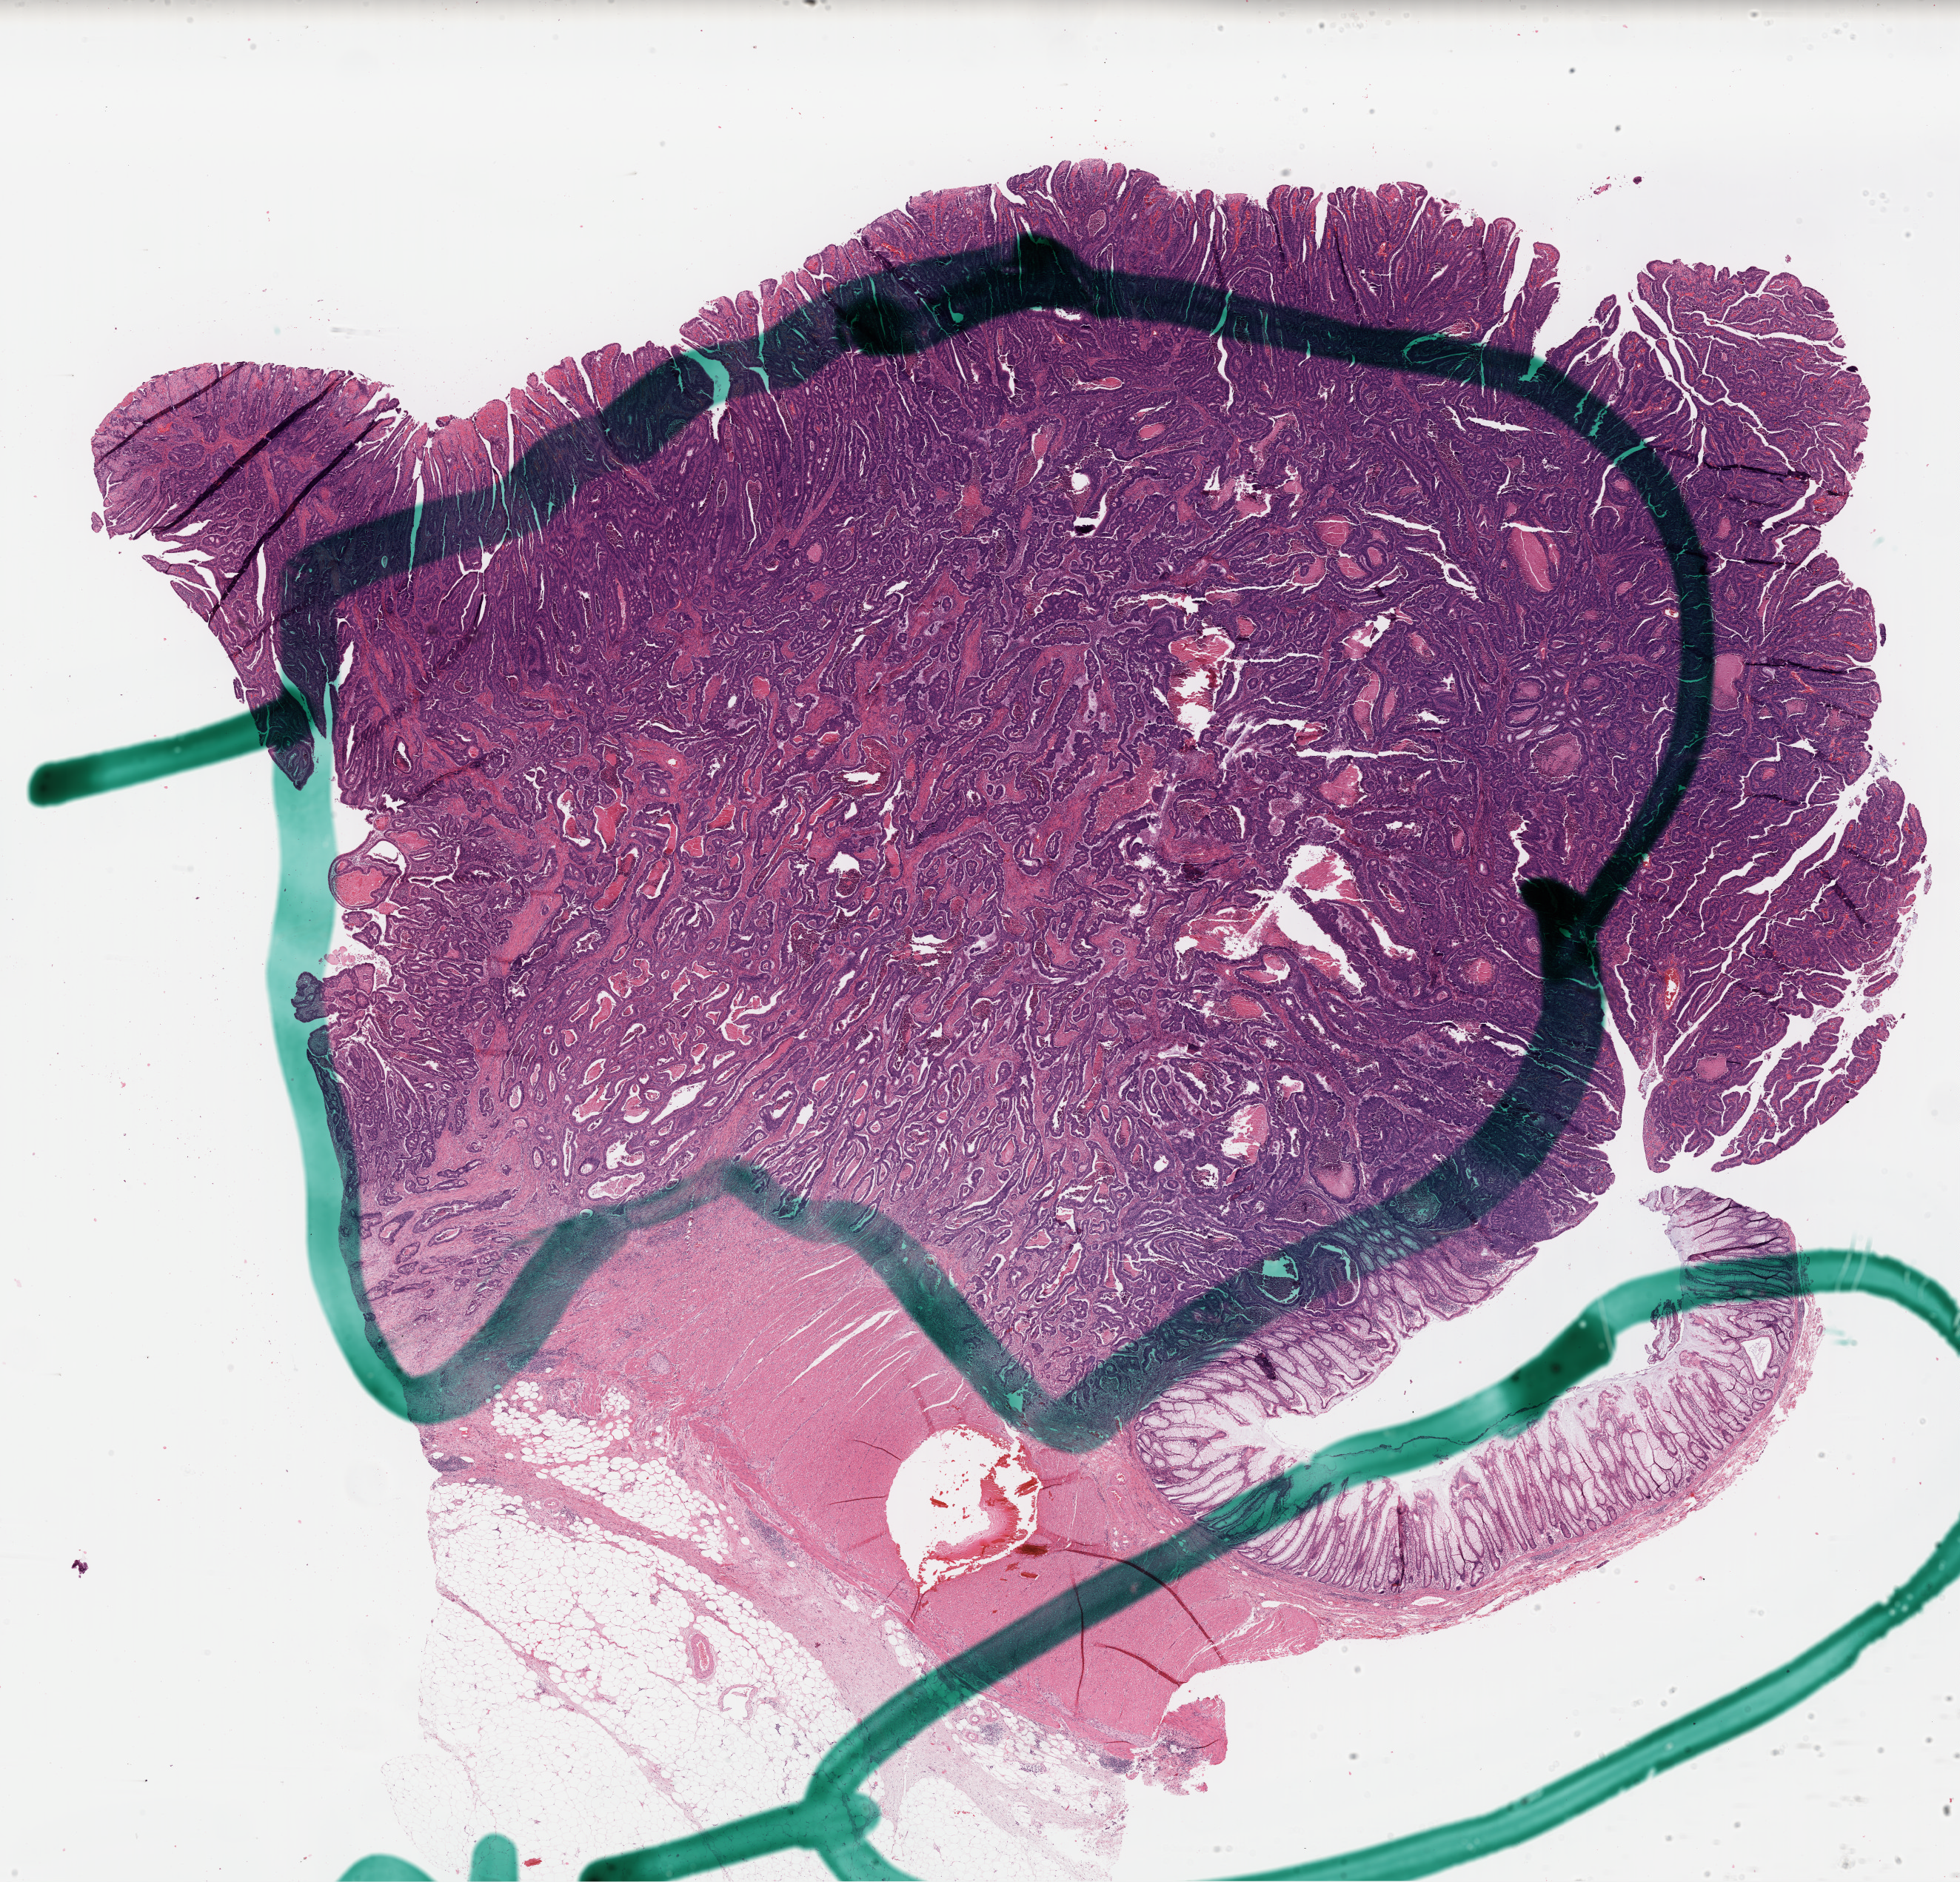
Whole-slide histology image, H&E, whole scanned area (about 20.9 x 20.1 mm) shown as a low-resolution overview, formalin-fixed paraffin-embedded (FFPE) diagnostic section, sample: primary tumour, colon. Female, age 72 years at initial diagnosis.
Diagnosis: Adenocarcinoma, NOS. Lymph nodes positive (case pathology): 0 of 15 examined. AJCC pathologic stage: IIA.